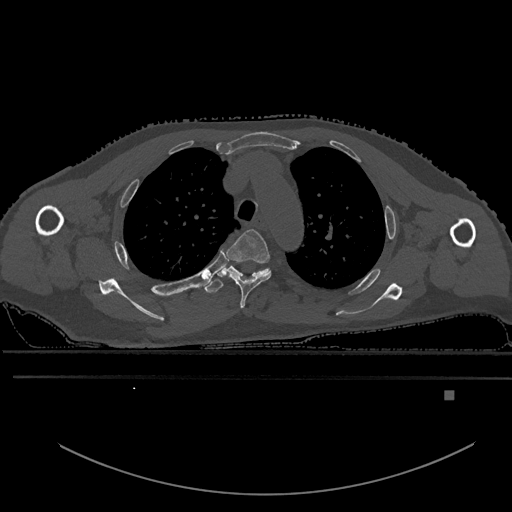
CT including the spine, one axial slice; position 436 of 969 along the scan axis; bone window (W 1800 / L 400 HU); 512 × 512 image matrix, field of view 456 × 456 mm. Patient: male, 82 years. From the clinical record (not read from this slice): primary cancer: prostate; vertebrae with lytic lesions (as recorded): T11, T9, T8, T2.
Outlined on this slice (semi-automatically segmented with operator editing):
- T3 vertebra: bounding box [x1, y1, x2, y2] px = [221, 229, 272, 309]
- T4 vertebra: [204, 264, 271, 293]